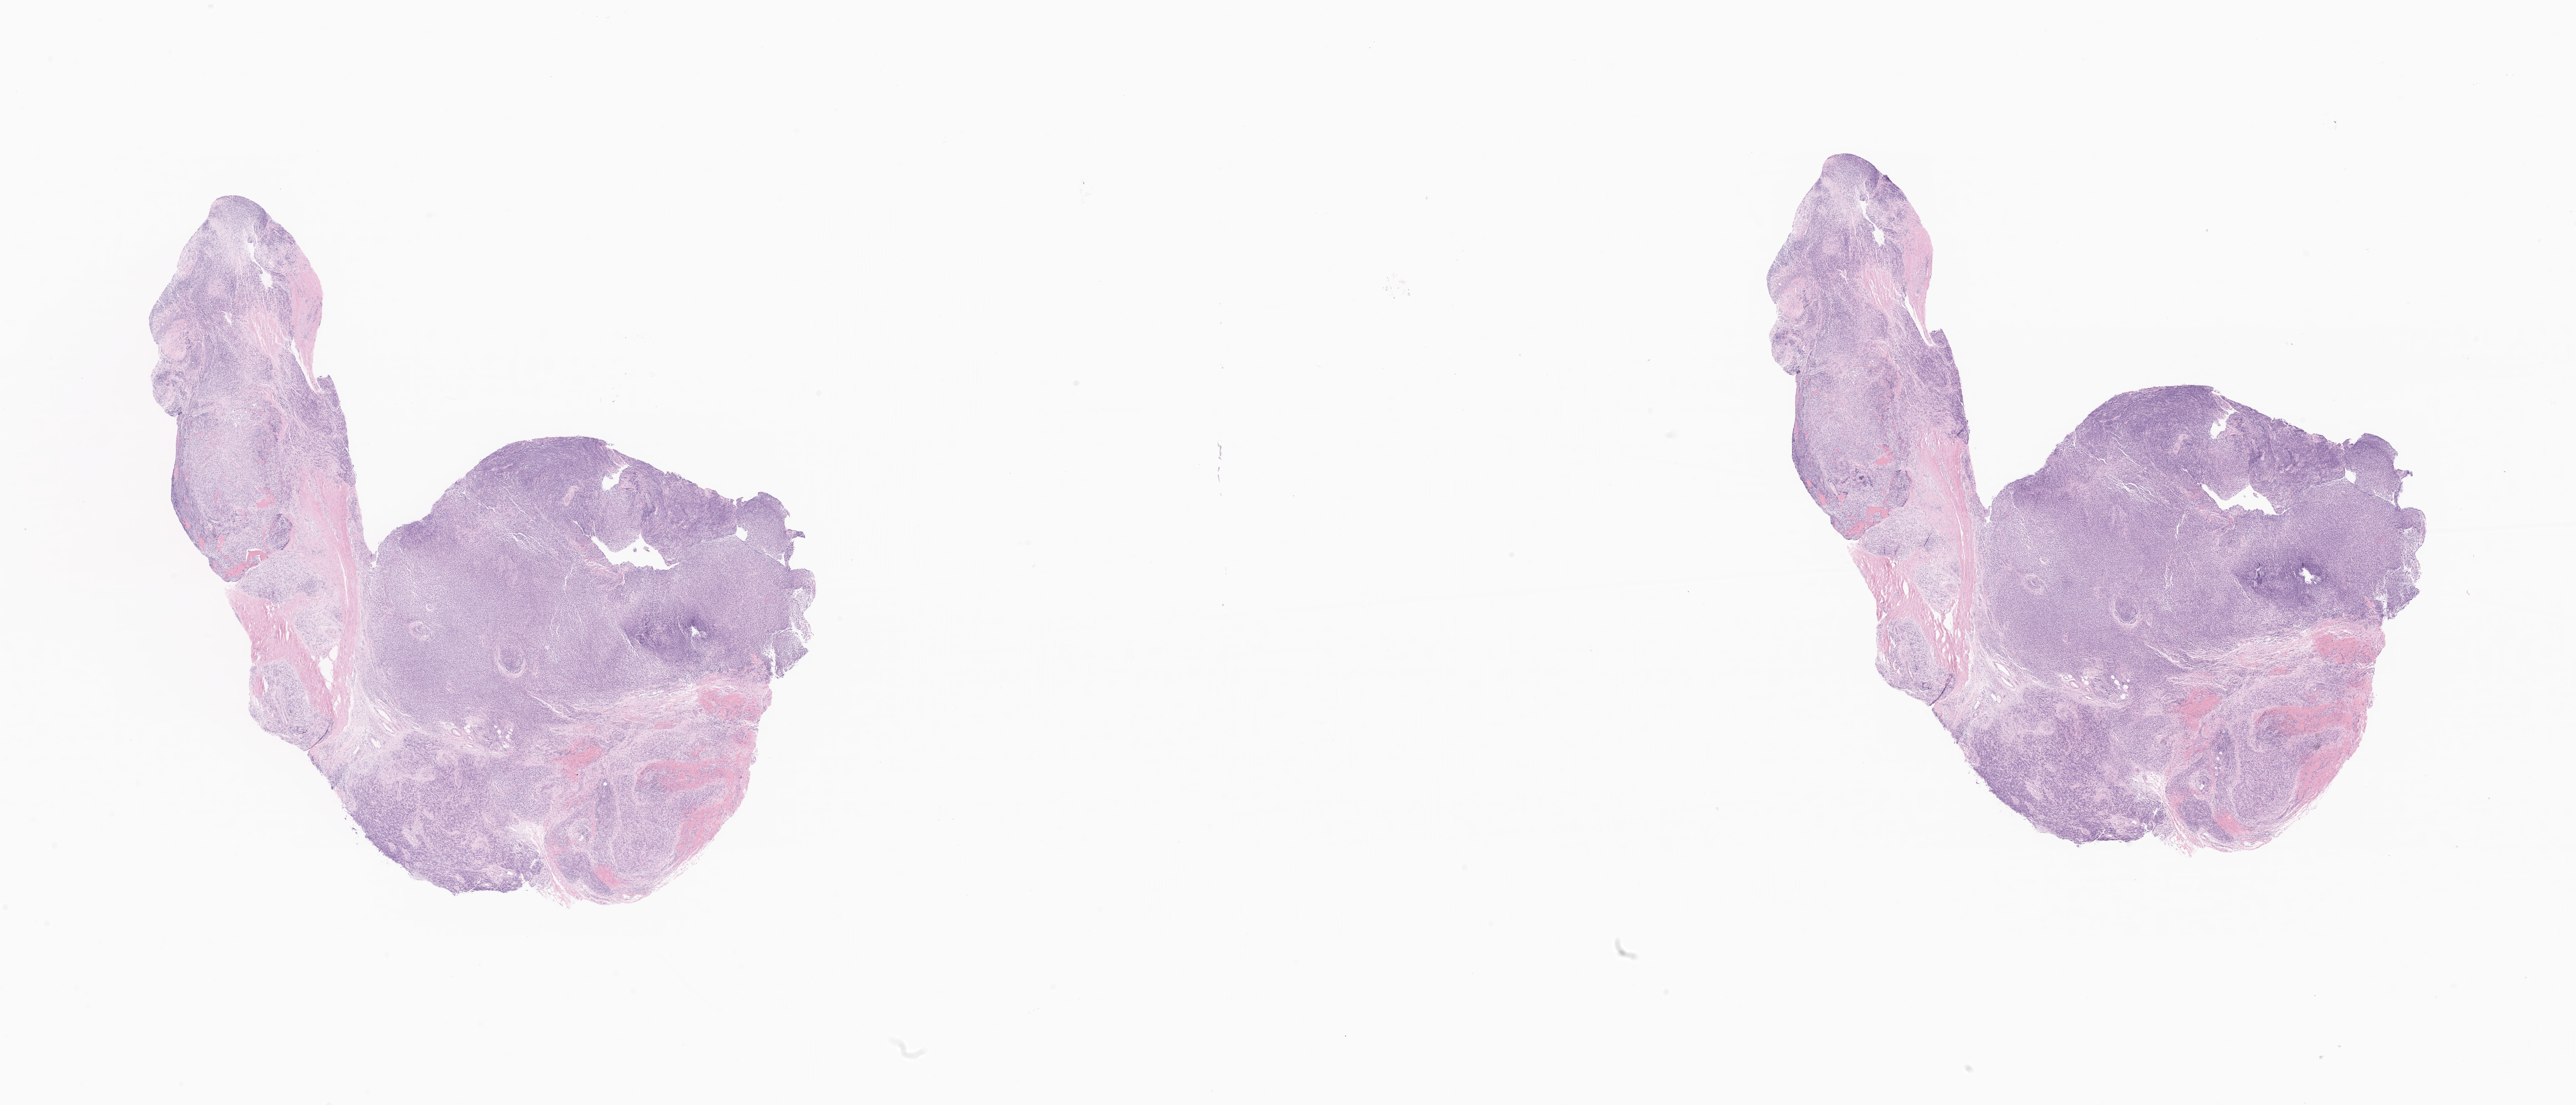
Digitized hematoxylin and eosin (H&E)-stained section of tumor tissue from the orbit, whole scanned area (about 31.6 x 13.6 mm) shown as a low-resolution overview; formalin-fixed paraffin-embedded section. Male patient, age 843 days.
Recorded diagnosis: Embryonal rhabdomyosarcoma, NOS.